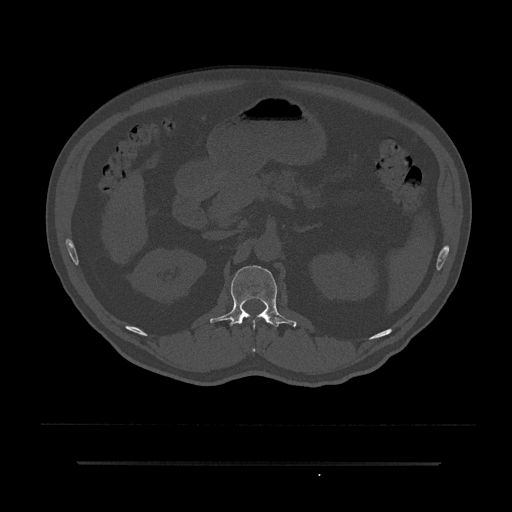
CT including the spine, one axial slice. Slice 153 of 797 in the series (ordered by position). Reconstruction kernel Br40s/3. 120 kVp. Bone window (W 1800 / L 400 HU). 0.5 mm slice thickness. 512 × 512 image matrix, field of view 464 × 464 mm. Patient: male, 59 years. Case-level facts recorded for this patient, not image findings: primary cancer: bile ducts; vertebrae with lytic lesions (as recorded): T10.
Outlined on this slice (semi-automatic segmentation, software-assisted and operator-edited):
- L1 vertebra: bounding box <210,265,297,351> (left, top, right, bottom; pixels)